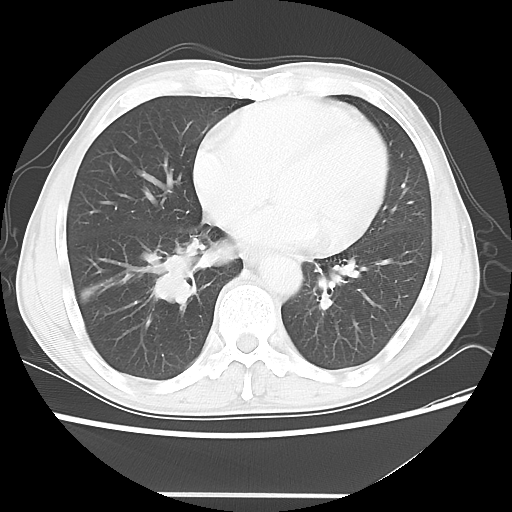
Chest CT, one axial slice. 120 kVp. Lung window (W 1500 / L -600 HU). 5 mm slice thickness. 512 × 512 image matrix. Male patient, age 65 years. Case-level facts recorded for this patient, not image findings: clinical TNM (as recorded): T1c N3 M0; histopathological grade: G3.
Outlined on this slice (bounding box drawn by a radiologist):
- lung tumour (recorded histology: small cell carcinoma): bounding box (x1, y1, x2, y2) in pixels: (146, 248, 202, 309)